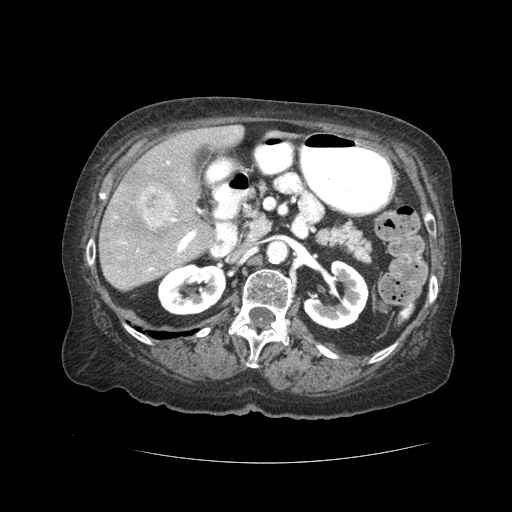
Contrast-enhanced abdominal CT (liver protocol), one axial slice. Slice 13 of 59 in the series (ordered by position). Soft-tissue window (W 400 / L 40 HU). 2.5 mm slice thickness. 512 × 512 image matrix. Case-level facts recorded for this patient, not image findings: diagnosis: hepatocellular carcinoma (patient treated with transarterial chemoembolisation; whether this scan precedes or follows treatment is not stated here); TNM stage (as recorded): Stage-I; Child-Pugh class: A; tumour nodularity: uninodular.
Annotated regions visible in this slice (semi-automatically segmented with operator editing):
- liver parenchyma outside the tumour (the mass and vessels are separate outlines, so this box may not span the whole liver): bounding box <98,124,244,290> (left, top, right, bottom; pixels)
- mass: <133,184,178,228>
- liver vessels: <123,130,238,271>